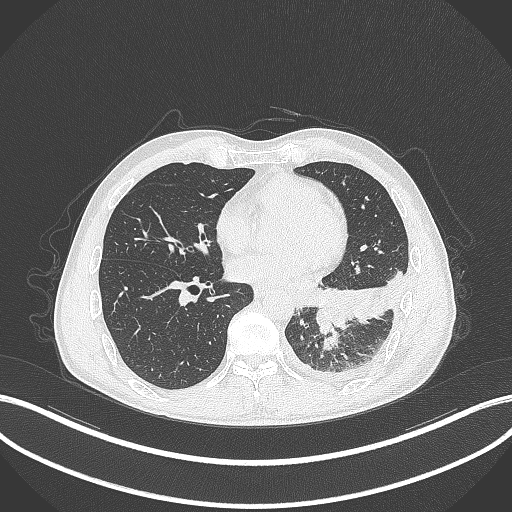
Chest CT, one axial slice. Position 126 of 295 along the scan axis. Reconstruction kernel B70f. 120 kVp. Lung window (W 1500 / L -600 HU). 512 × 512 image matrix, field of view 400 × 400 mm. Male patient, age 47 years. From the clinical record (not read from this slice): clinical TNM (as recorded): T3 N1 M1c.
Annotated regions visible in this slice (rectangle marked by the reading radiologist):
- lung tumour (recorded histology: small cell carcinoma): bounding box [x1, y1, x2, y2] px = [317, 285, 354, 335]